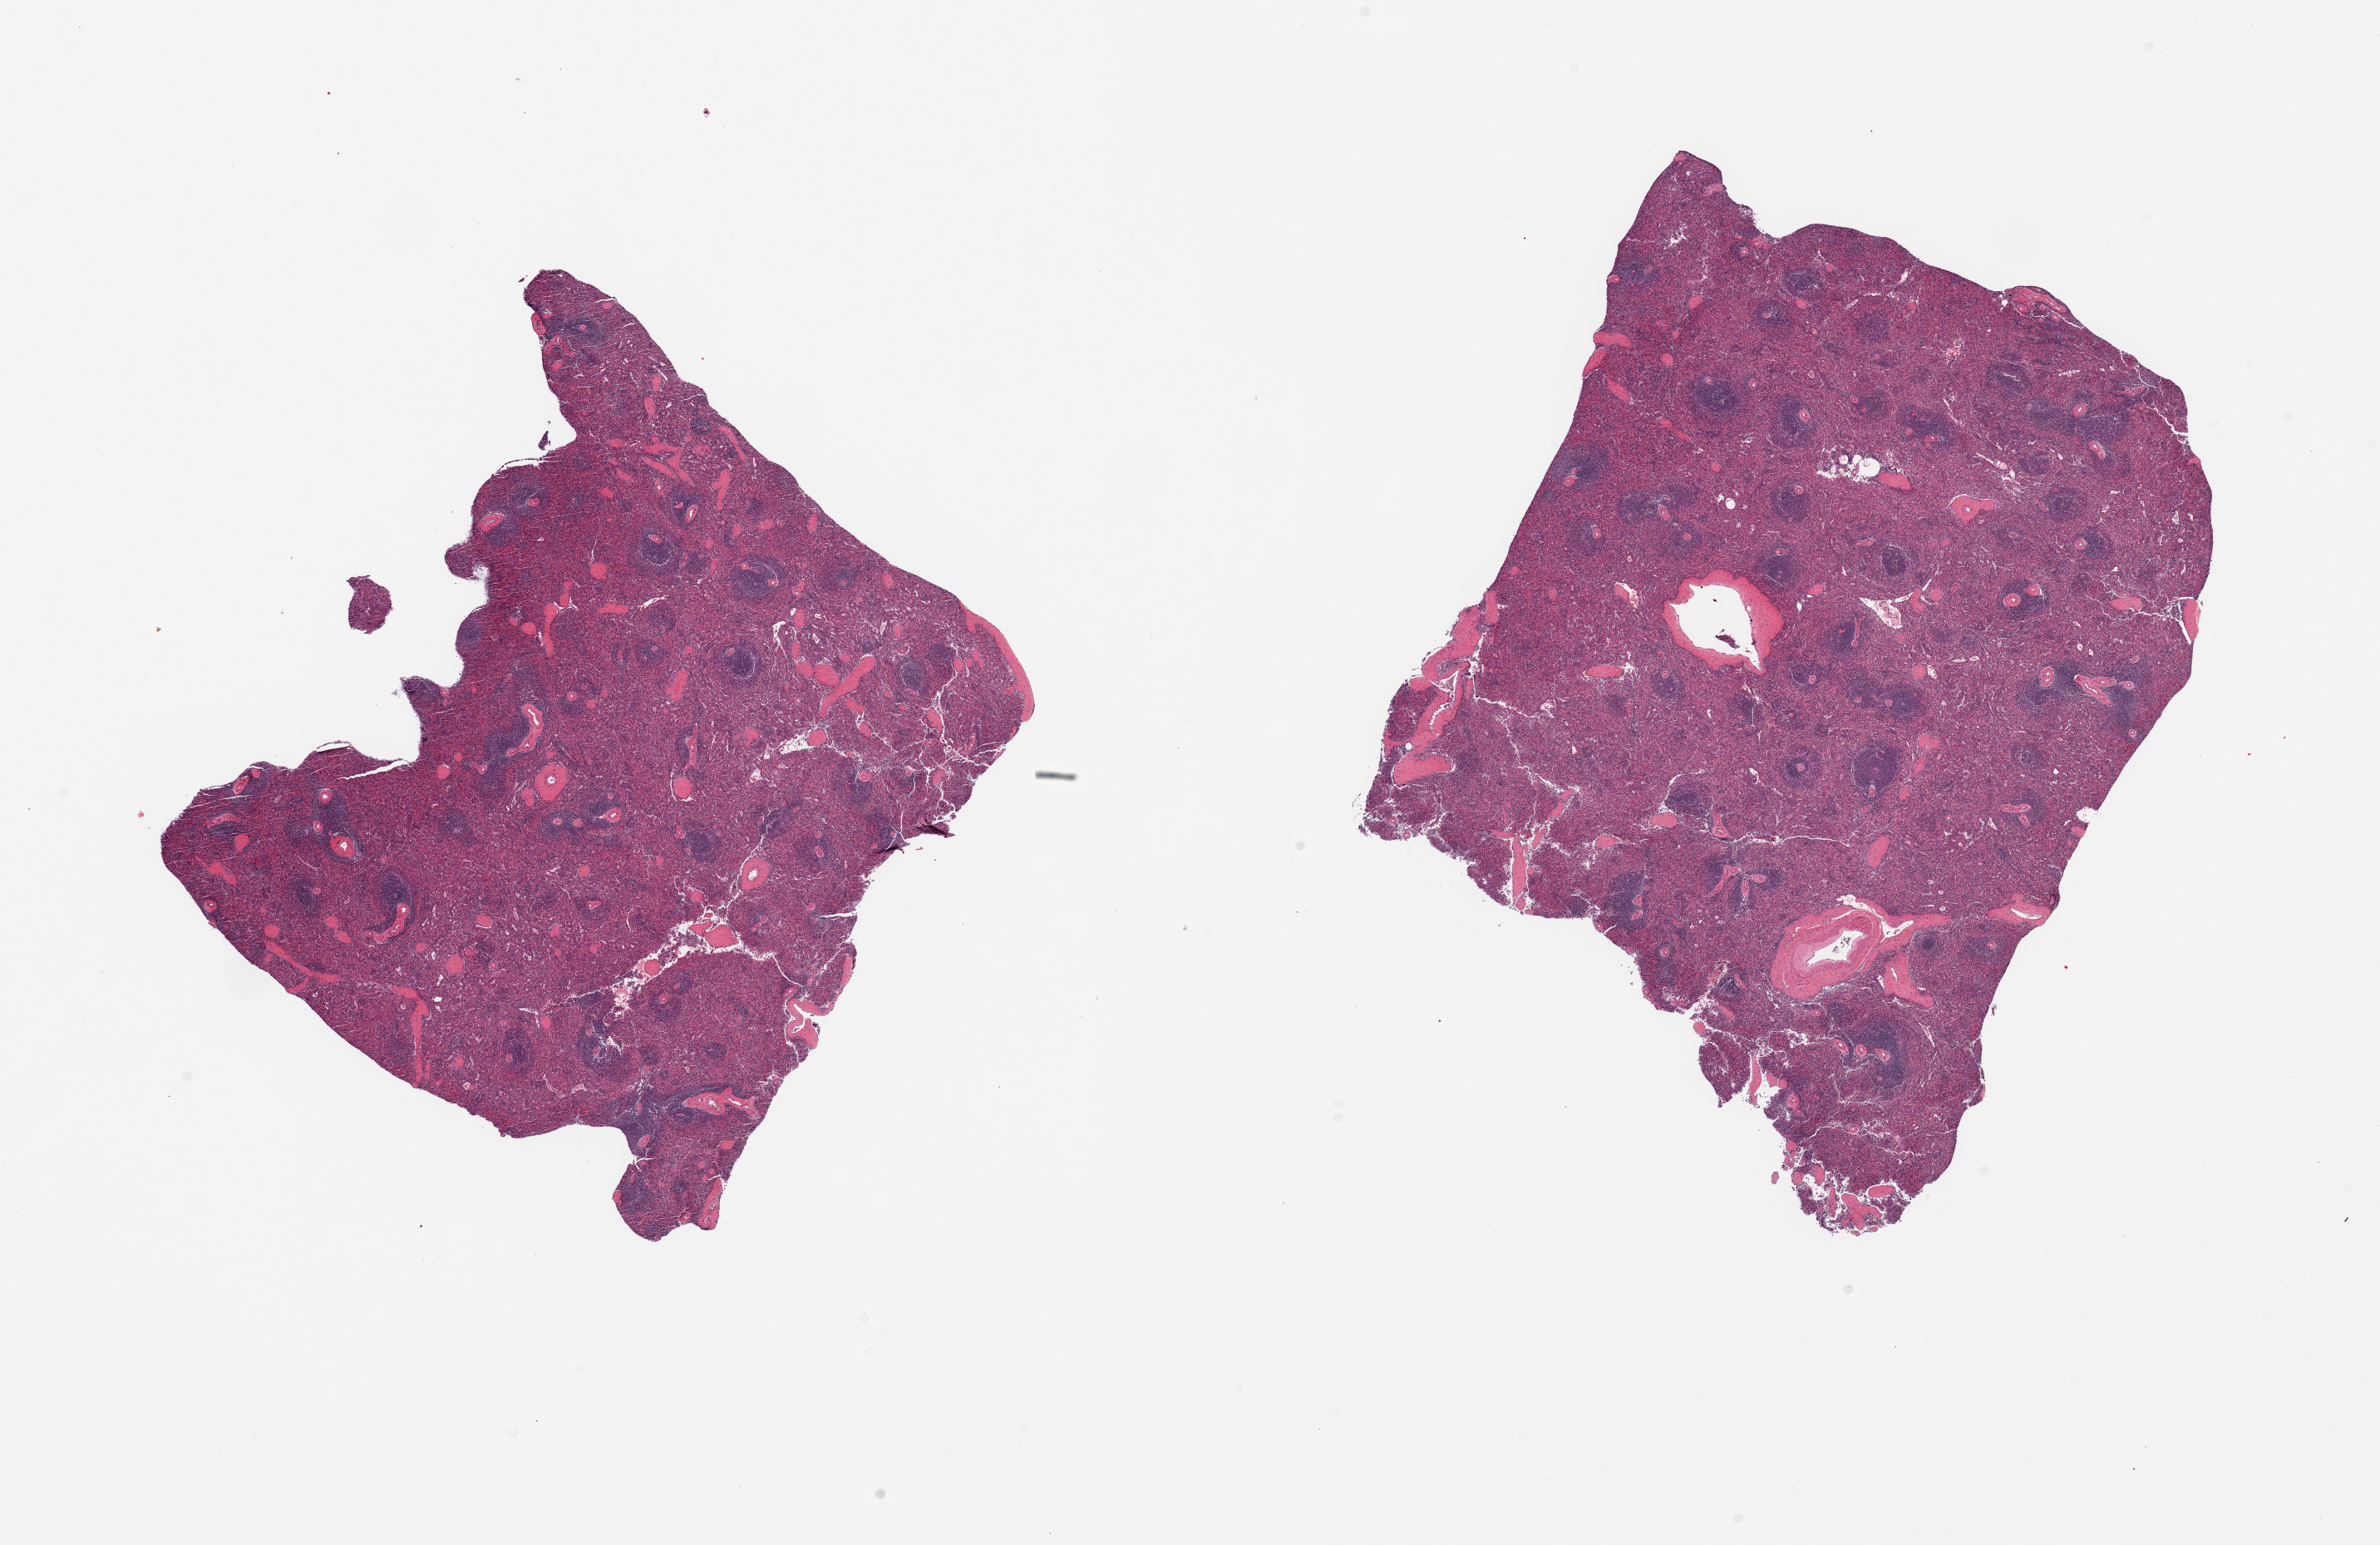
H&E whole-slide image — low-resolution overview of the scanned area, about 22.6 x 14.7 mm; PAXgene-fixed, paraffin-embedded tissue; target tissue: spleen; tissue donor sample. Donor sex: female.
* pathologist's review note for this sample: 2 pieces